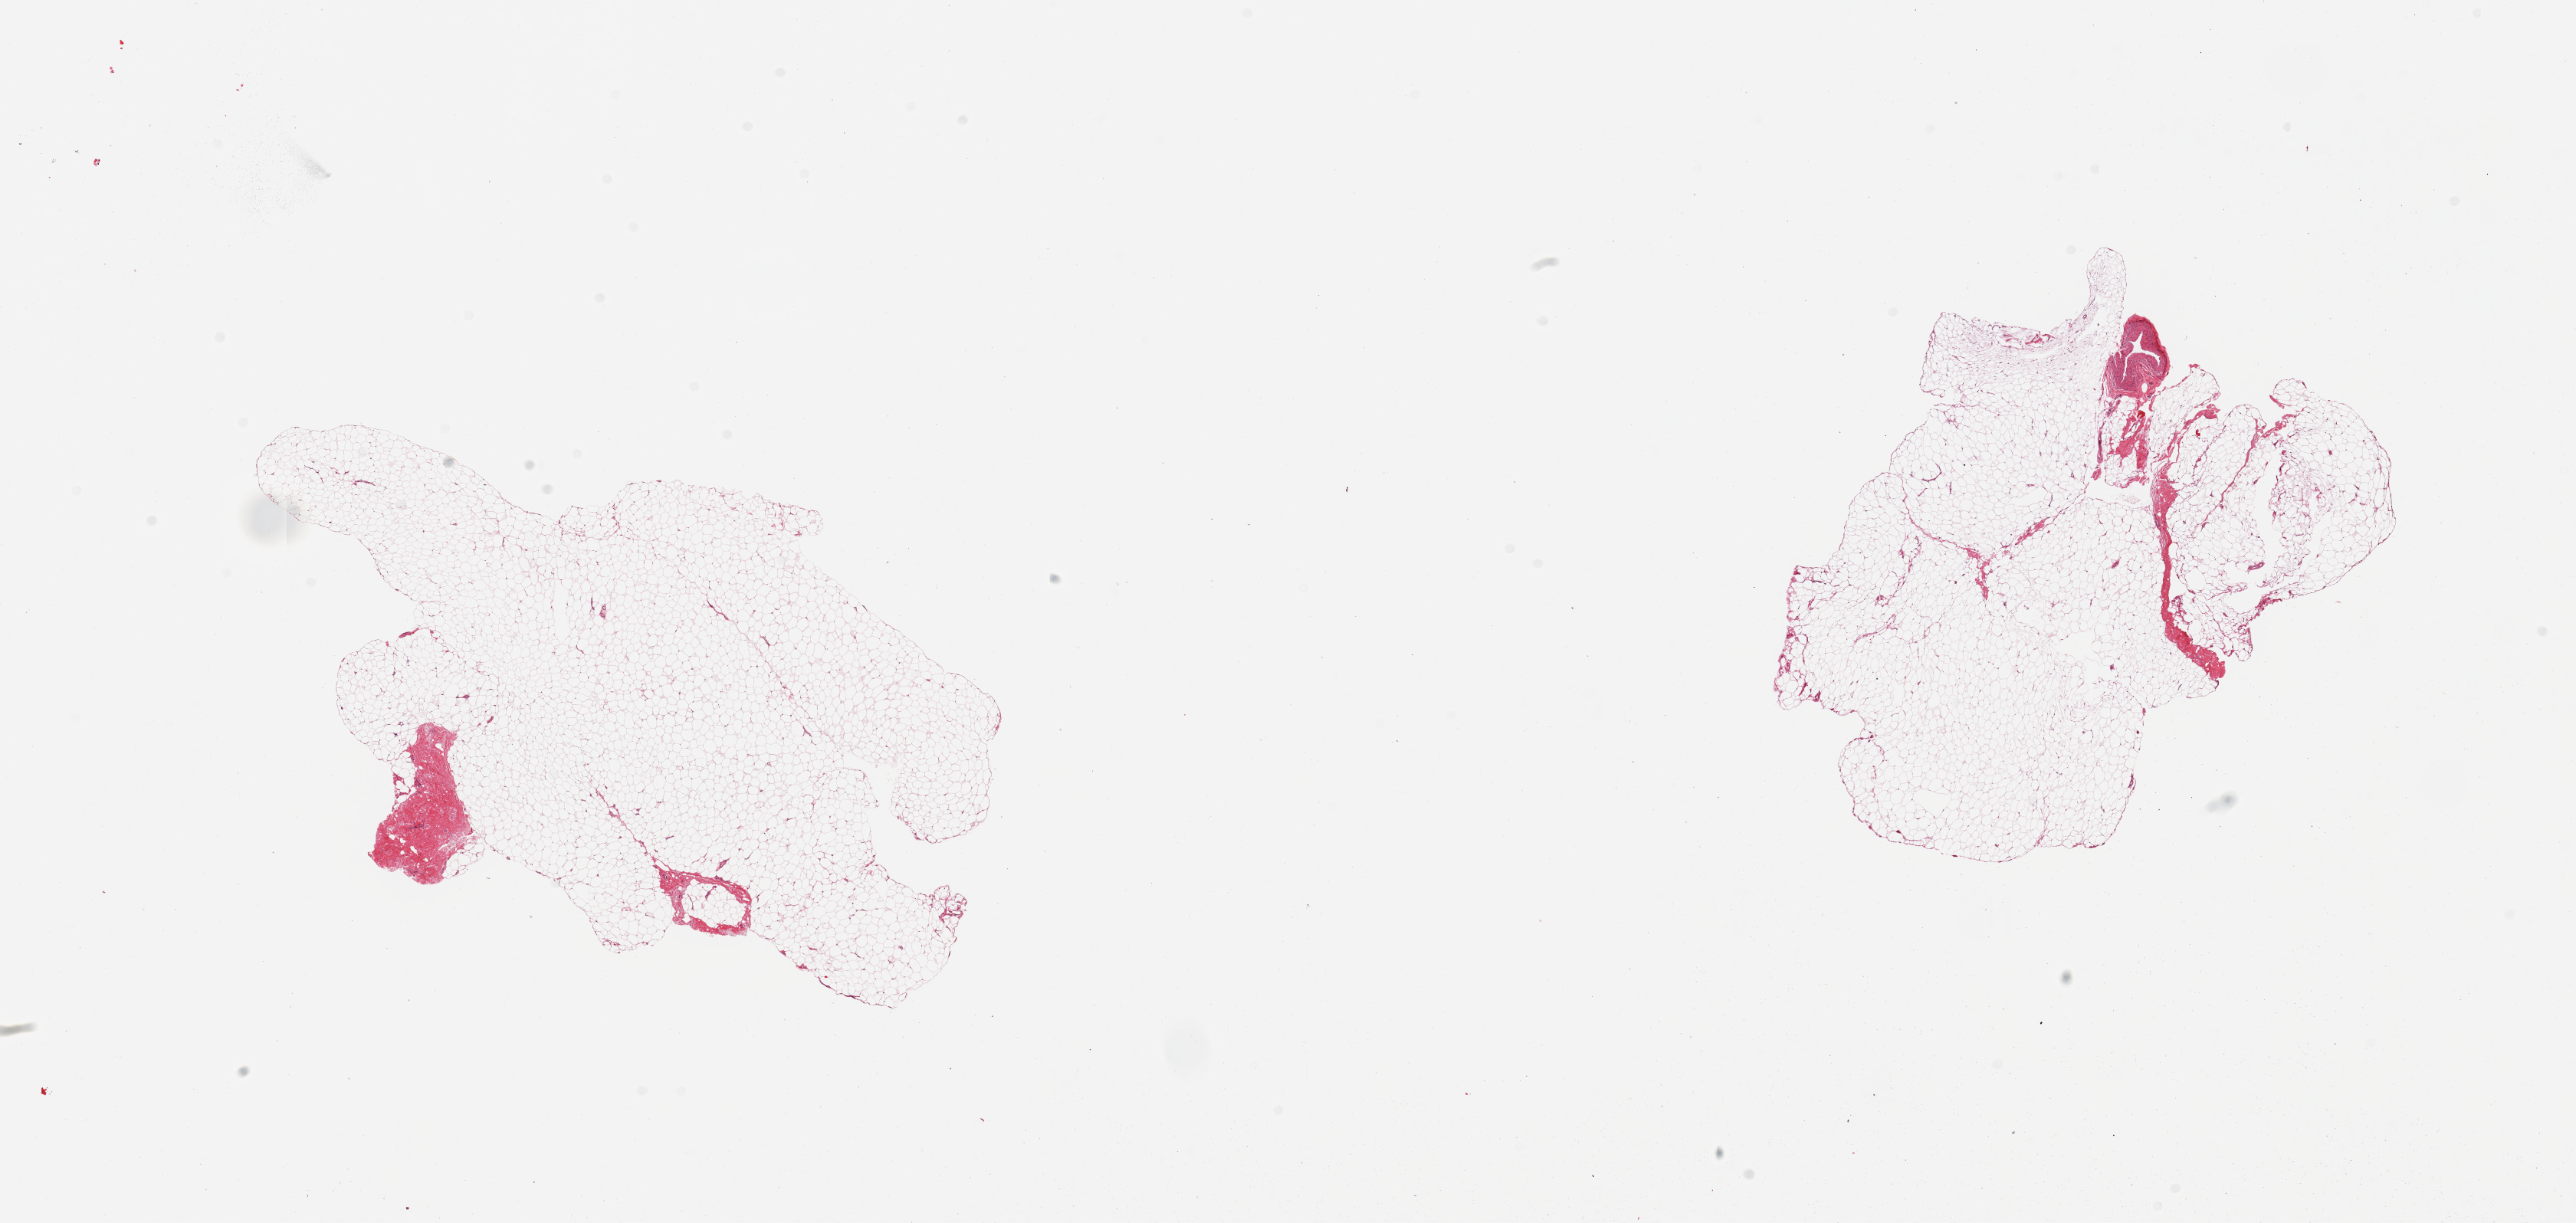
Digitized haematoxylin and eosin-stained section, shown as a low-resolution overview of the whole scanned area (about 26.6 x 12.6 mm); PAXgene-fixed, paraffin-embedded tissue; section of adipose tissue (target tissue); tissue donor sample. Male donor.
- pathologist's review note for this sample: 2 pieces